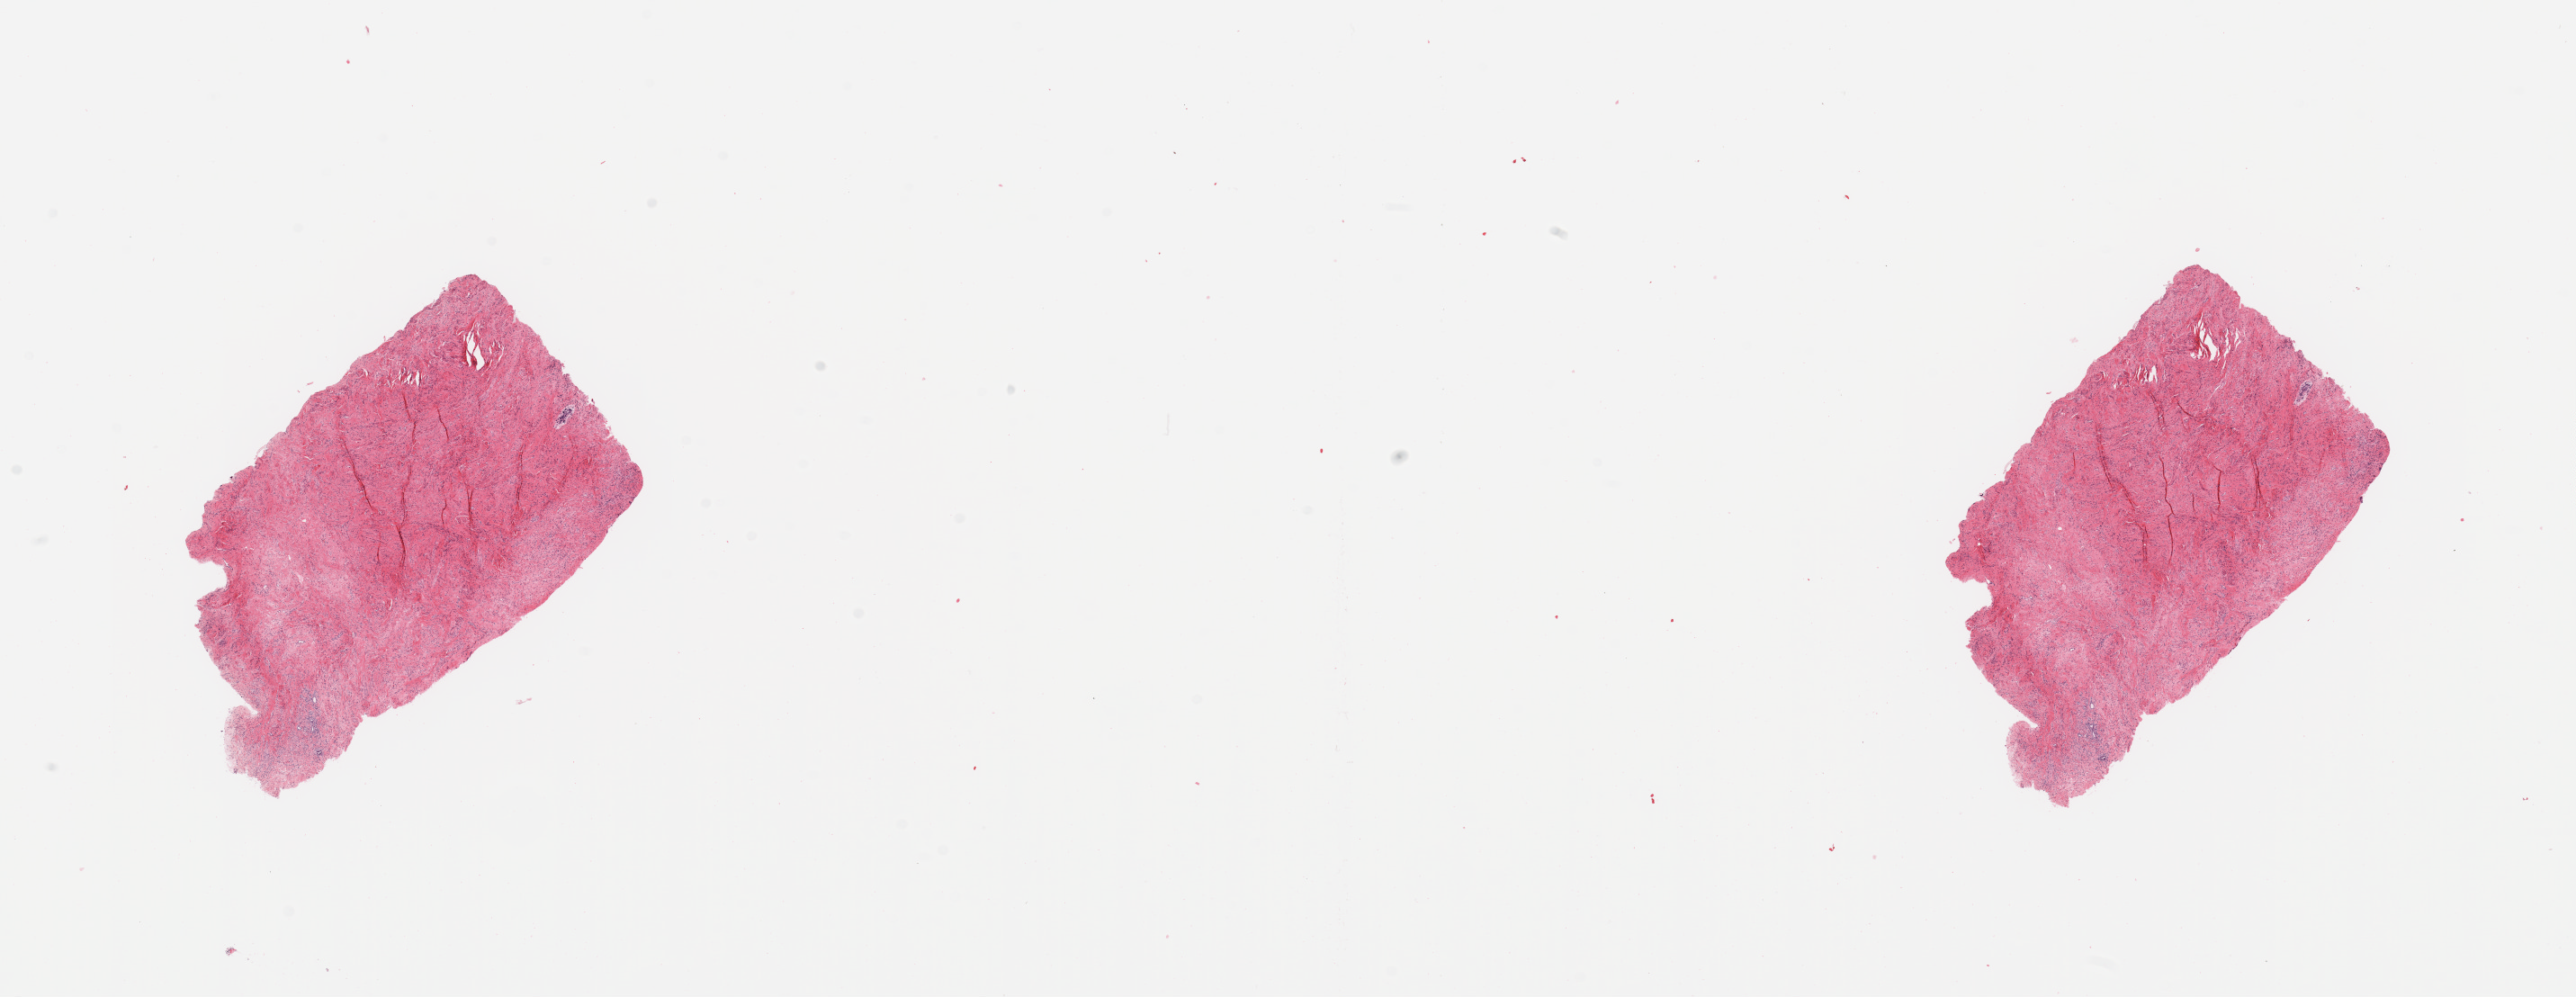
H&E-stained whole-slide image — low-resolution overview of the scanned area, about 22.6 x 8.8 mm. Uterus, normal (non-tumour) tissue. Patient: female, age 86 years.
This section: normal (non-tumour) tissue from the same patient. Patient diagnosis: Endometrioid adenocarcinoma, NOS.